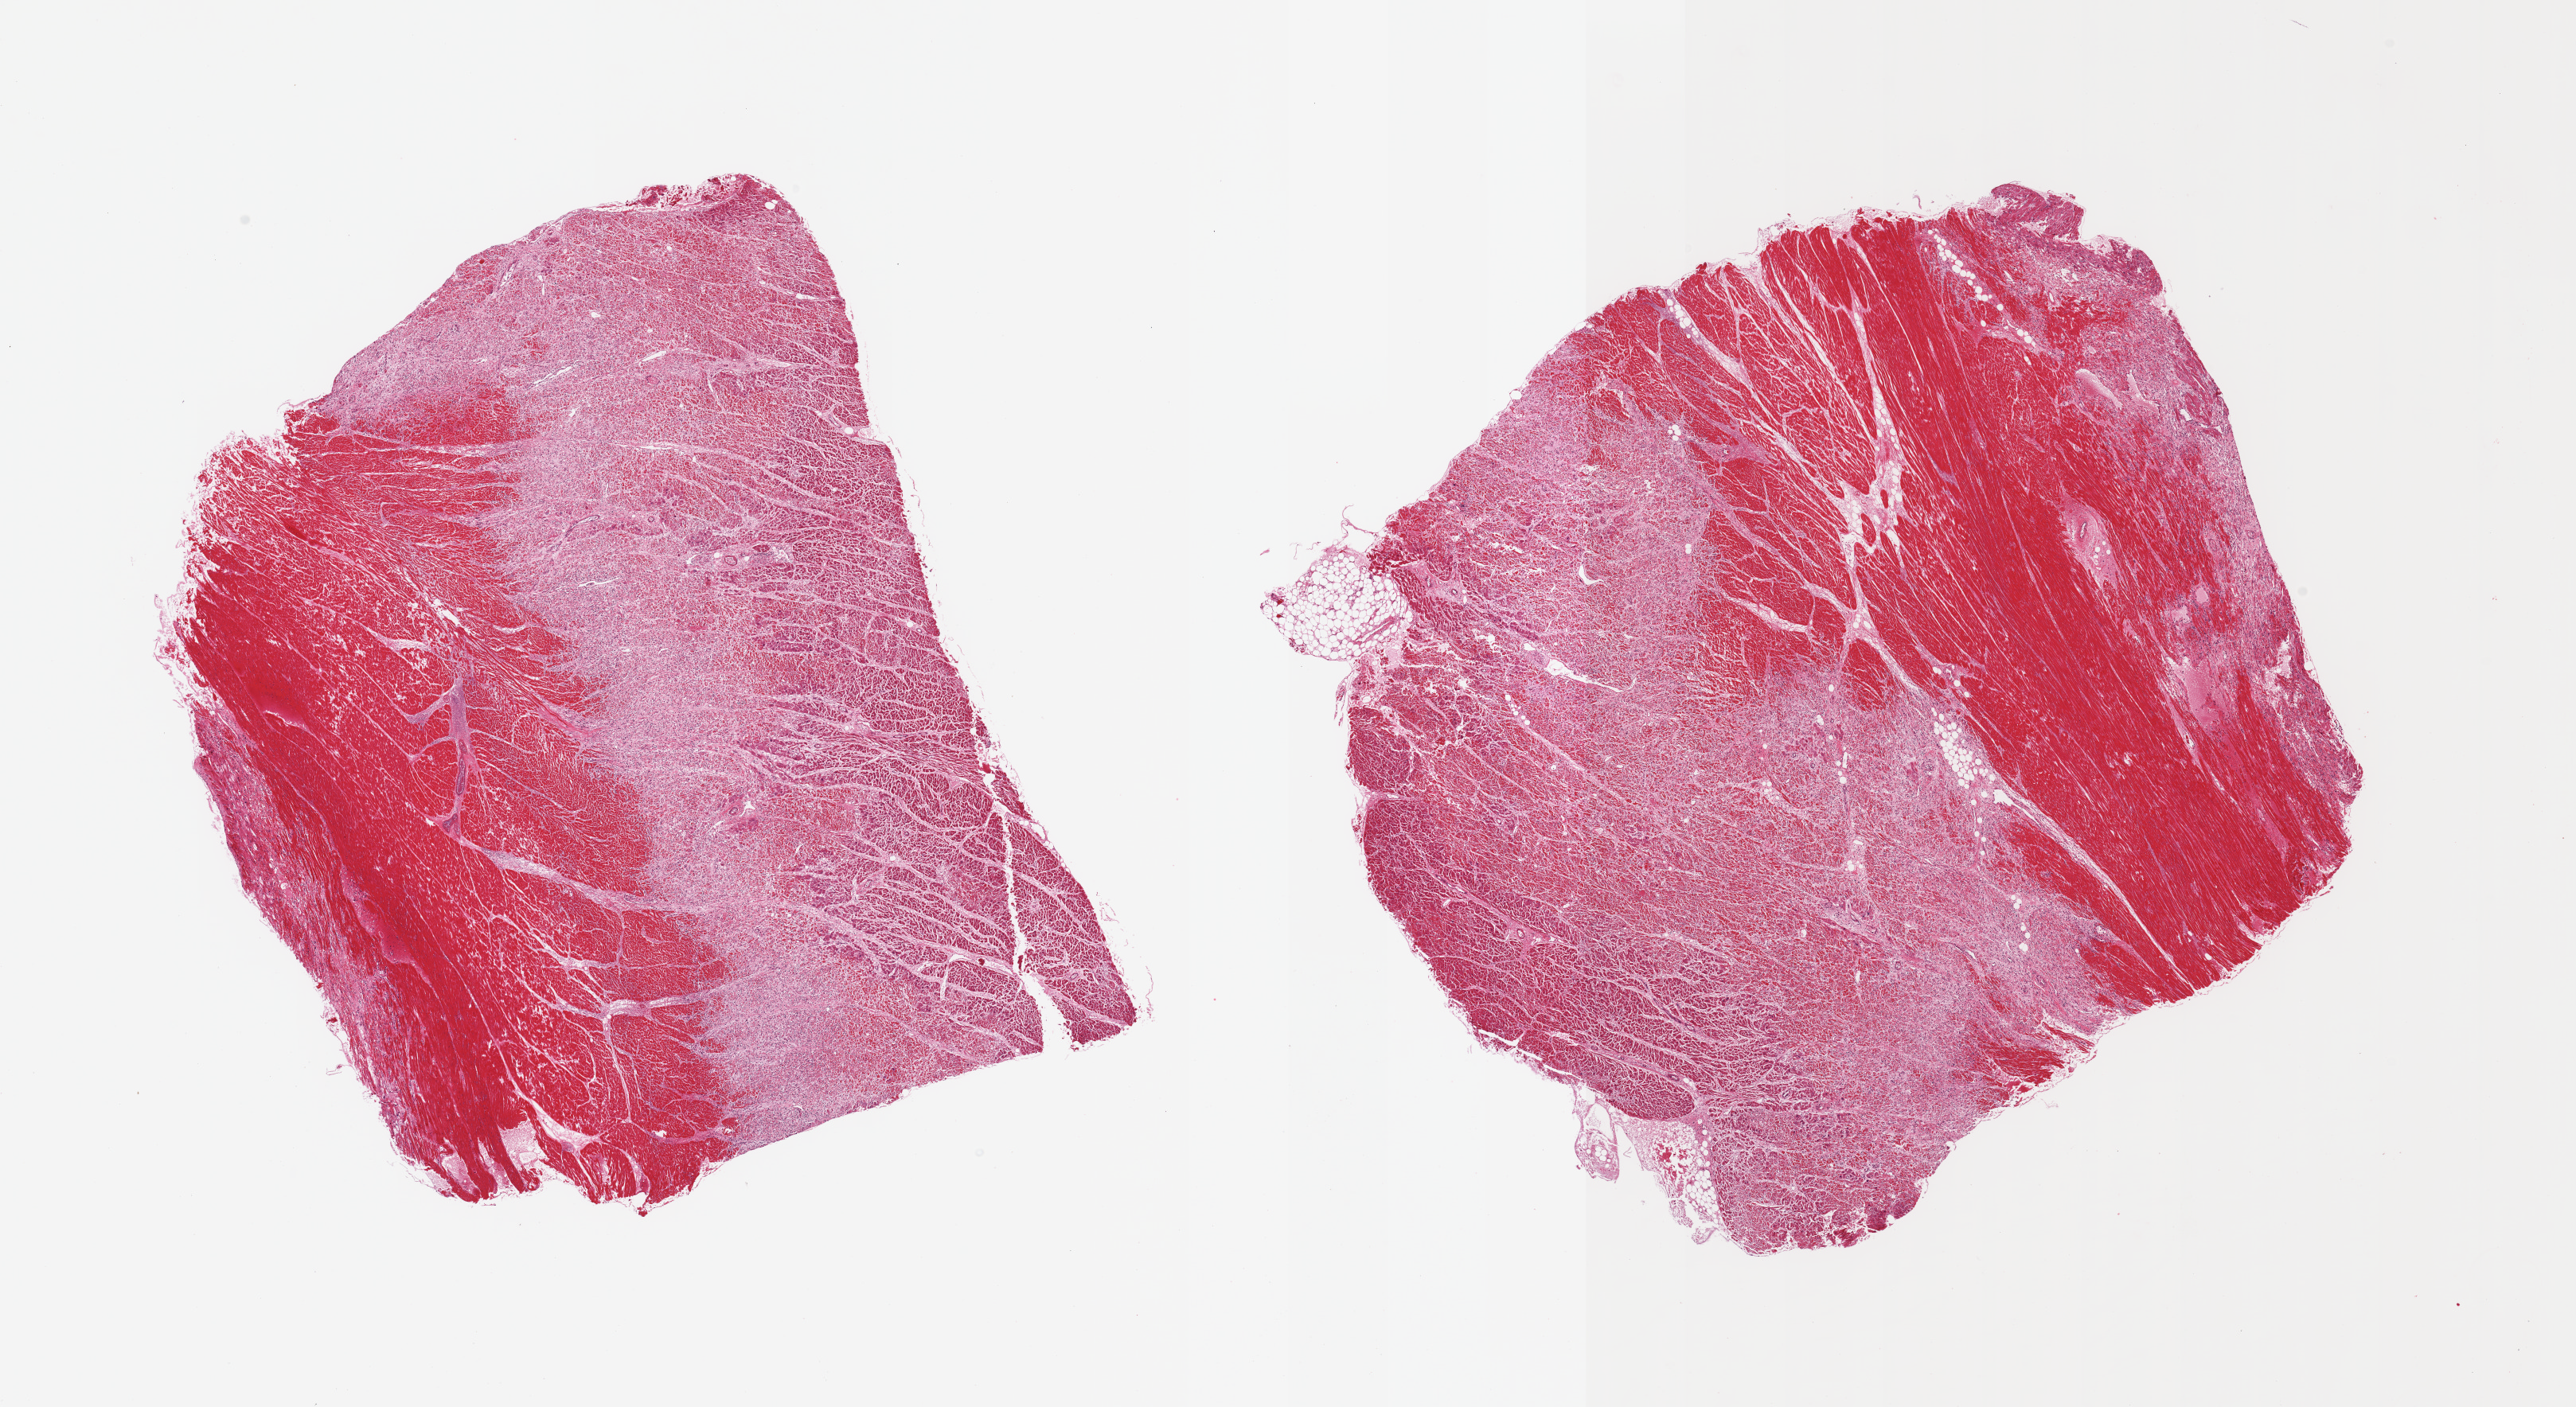
H&E whole-slide image, brightfield, whole scanned area (about 25.6 x 14.0 mm) shown as a low-resolution overview. Donor: male.
Specimen: PAXgene-fixed paraffin-embedded (PFPE) section; target tissue: heart; donor tissue sample.